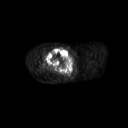
FDG PET of an extremity soft-tissue mass (from a PET/CT study), one axial slice. Position 262 of 311 along the scan axis. 3.27 mm slice thickness. 128 × 128 image matrix. Patient: male, 50 years. Case-level facts recorded for this patient, not image findings: histological type: undifferentiated - pleiomorphic; grade: high; site of the primary tumour: right thigh.
Structures marked on this image (expert contour drawn on MRI and transferred to this co-registered scan by the dataset authors):
- gross tumour volume including surrounding oedema: box from (x=44, y=47) to (x=66, y=69) px
- gross tumour volume (mass): (x=46, y=48)–(x=66, y=68)